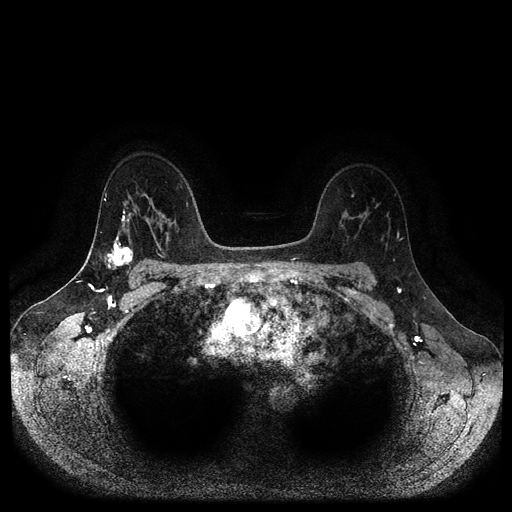
Breast MRI (dynamic contrast-enhanced, multi-phase), one axial slice. Position 71 of 116 along the scan axis. Dynamic contrast-enhanced series, time point 2 of 5 at this slice position (early post-contrast). 1.5 T. TE 2.6 ms, TR 5.3 ms. 512 × 512 image matrix, field of view 360 × 360 mm. Female patient, age 45 years.
Outlined on this slice (semi-automatically segmented with operator editing):
- breast lesion (labelled 'tumour' in the annotation; benign lesions carry a separate 'benign' label): bounding box <105,233,135,271> (left, top, right, bottom; pixels)